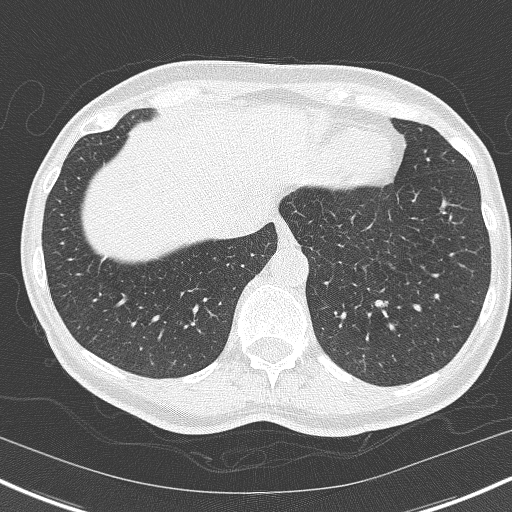
Axial slice from a low-dose chest CT screening exam. Second annual screen. Lung window (W 1500 / L -600 HU). 2 mm slice thickness. 120 kVp. Slice 137 of 171 in the series. 512 × 512 image matrix, field of view 318 × 318 mm. Female, age 55 years at enrolment. Current smoker at enrolment.
• Expert reader's lesion annotation, box from (x=358, y=285) to (x=402, y=325) px.
• Screening reader's record for this exam (one nodule recorded; not confirmed to be the boxed lesion): non-calcified nodule or mass ≥4 mm, right upper lobe, 13 × 6 mm, poorly defined margins, soft tissue attenuation, pre-existing on the prior screen: yes; interval growth: no.
• Note: the box lies in the patient's left hemithorax on this image, whereas the reader's record names the right lung; they may be different findings.
• Official screen result: positive, no significant change: stable abnormalities potentially related to lung cancer, unchanged since the prior screening exam.
• Lung cancer was diagnosed 700 days after this screen (after the third annual screen): adenocarcinoma, NOS, left lower lobe, well differentiated (G1), stage IA (AJCC 6th edition), 11 mm at pathology.